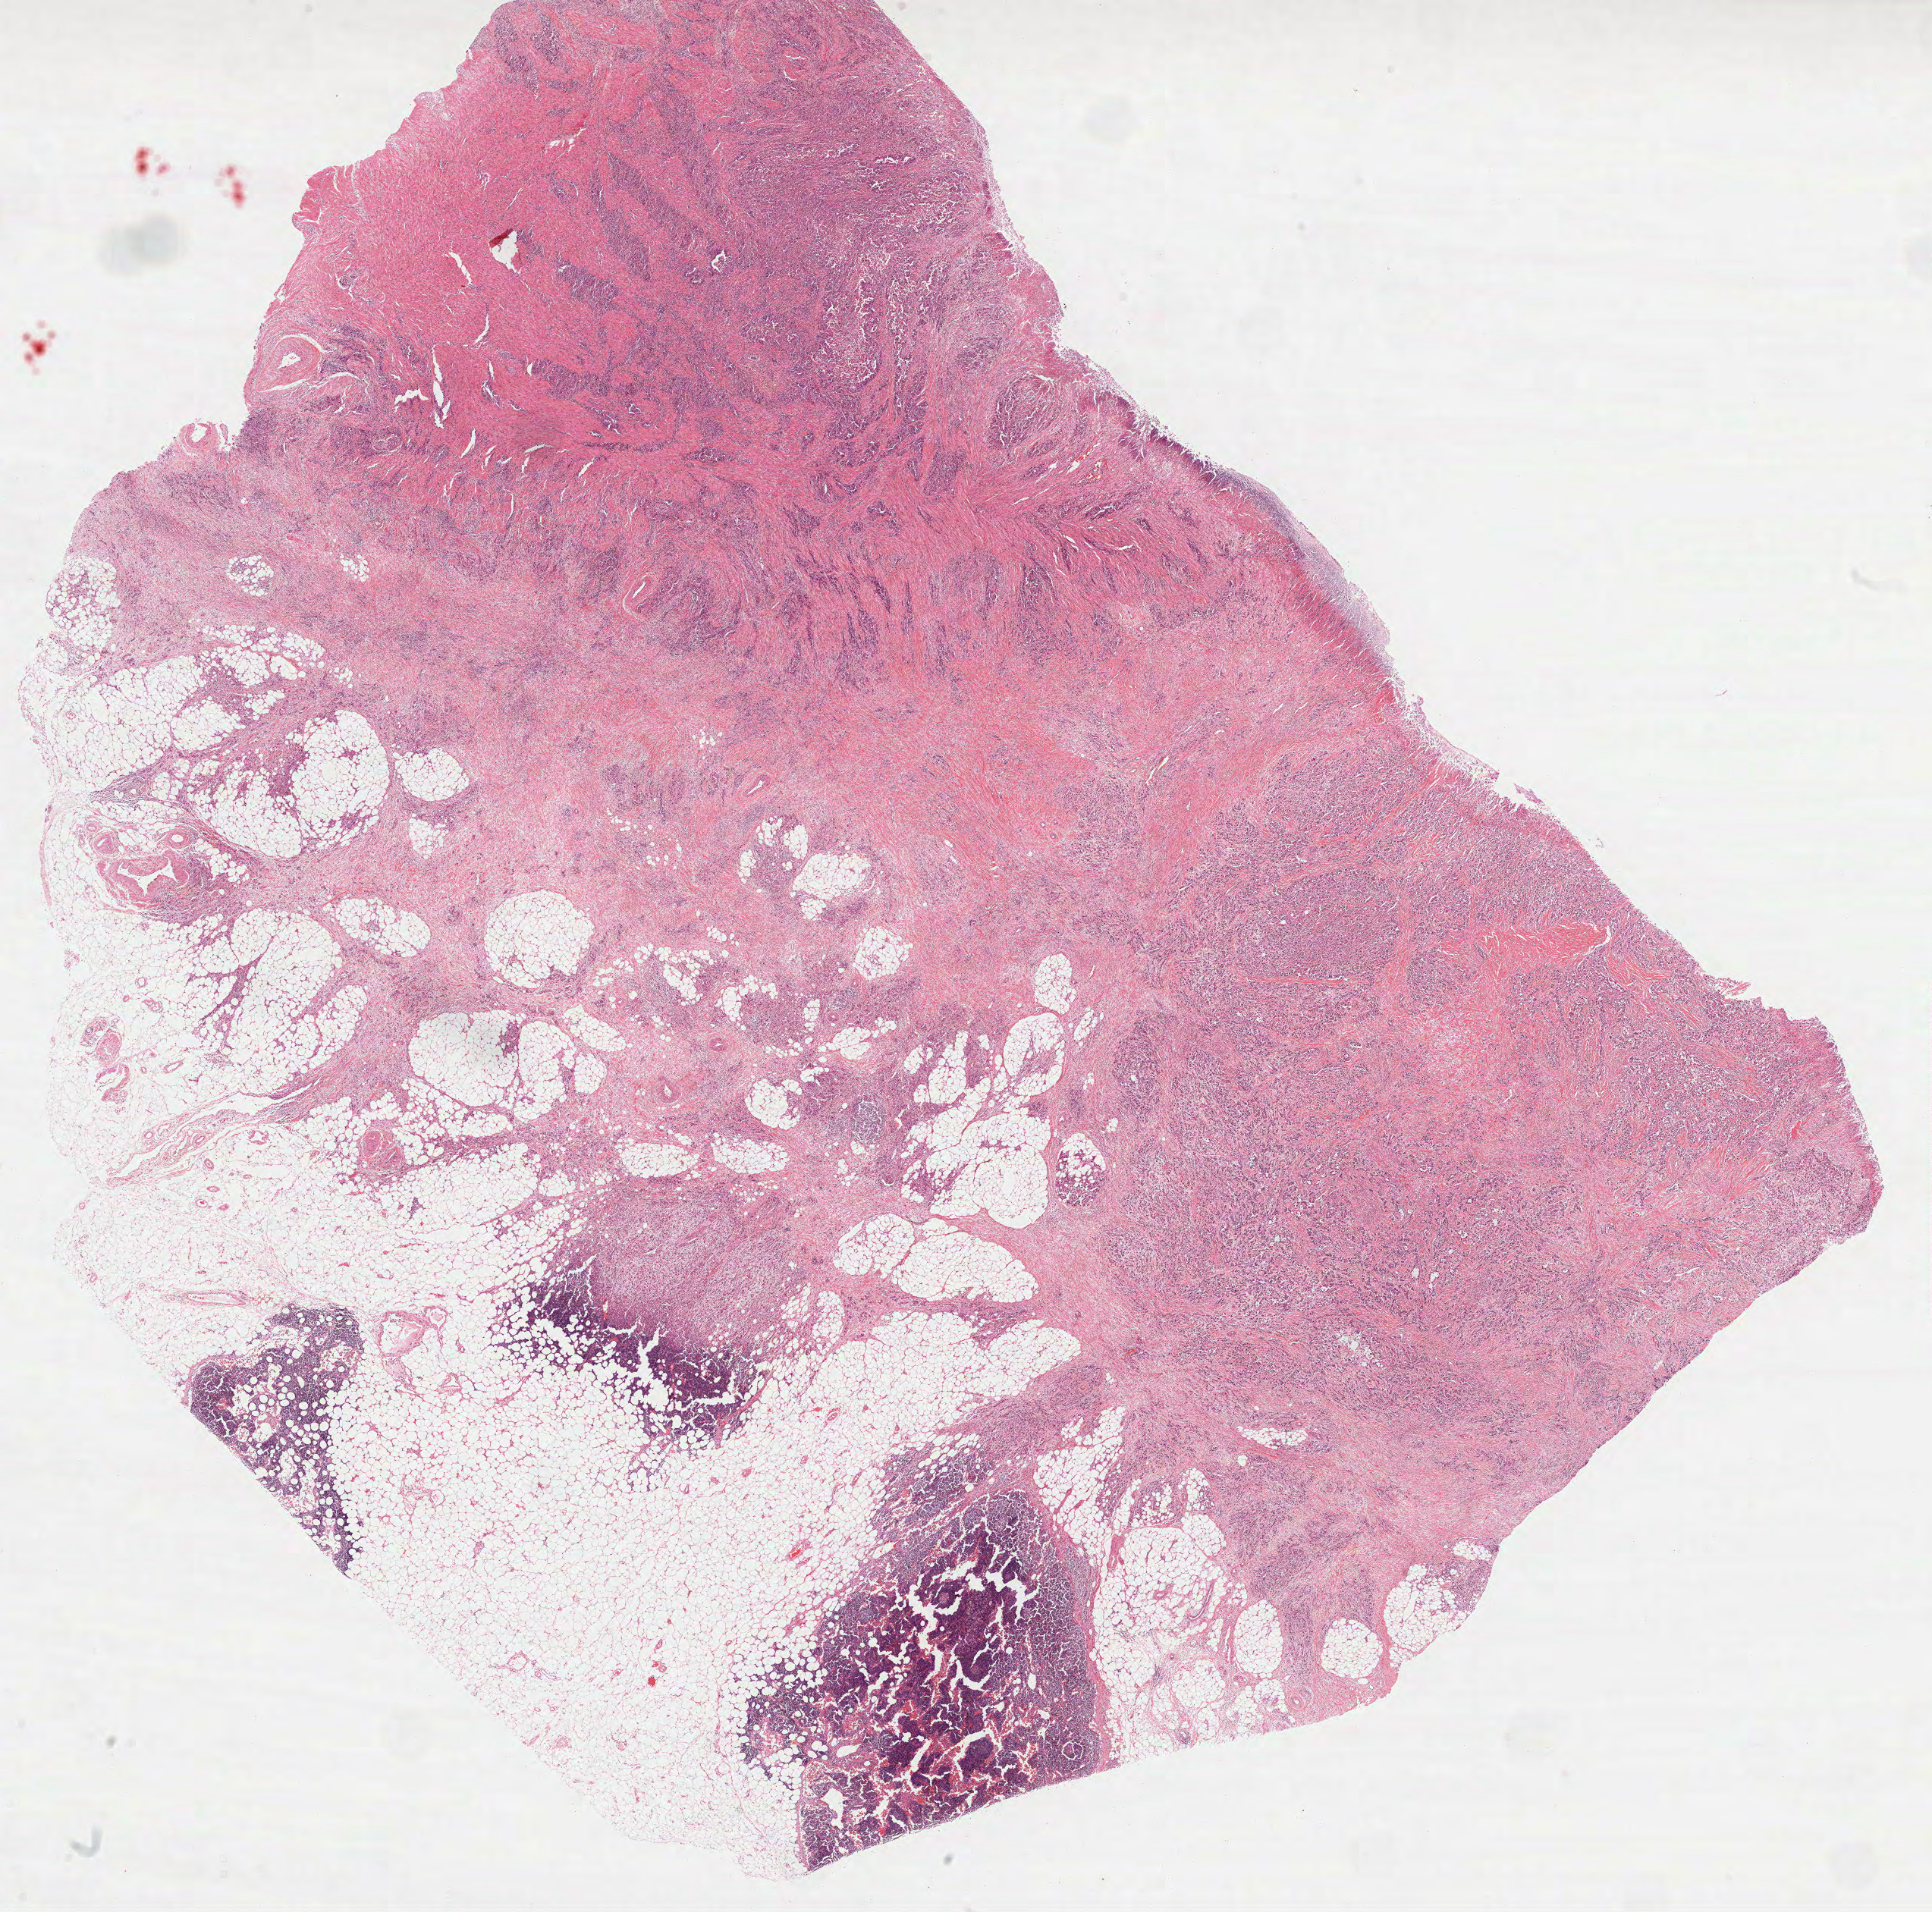
Whole-slide histology image, H&E-stained — whole scanned area (about 20.5 x 20.3 mm, acquisition: 40x scan) shown as a low-resolution overview. Formalin-fixed paraffin-embedded (FFPE) diagnostic section. Stomach, primary tumour sample. Female, age 74 years at initial diagnosis. Histologic grade: G3 (poorly differentiated).
• lymph nodes positive (case pathology): 8 of 15 examined
• histologic diagnosis: Adenocarcinoma, NOS (gastric antrum)
• AJCC pathologic stage: IIIB (7th edition)